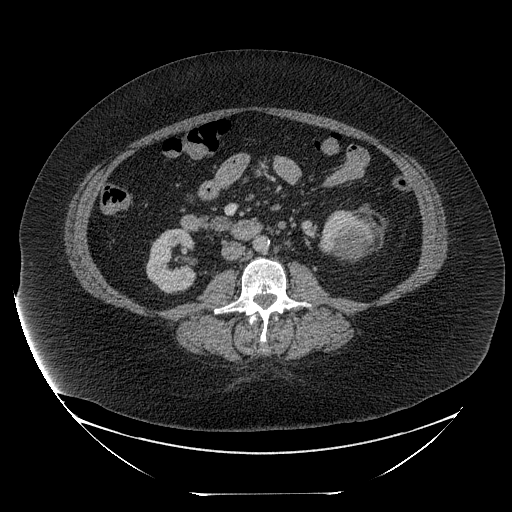
Contrast-enhanced abdominal CT, one axial slice. Position 110 of 205 along the scan axis. Reconstruction kernel STANDARD. 120 kVp. Soft-tissue window (W 400 / L 40 HU). 2.5 mm slice thickness. 512 × 512 image matrix, field of view 500 × 500 mm. Female patient, age 53 years. From the clinical record (not read from this slice): diagnosis: adrenocortical carcinoma; tumour side: left adrenal; tumour size at pathology: 17 cm; Ki-67 index: 20 %; stage (as recorded): 3.
Outlined on this slice (semi-automatically segmented with operator editing):
- mass: bounding box (x1, y1, x2, y2) in pixels: (334, 232, 374, 258)